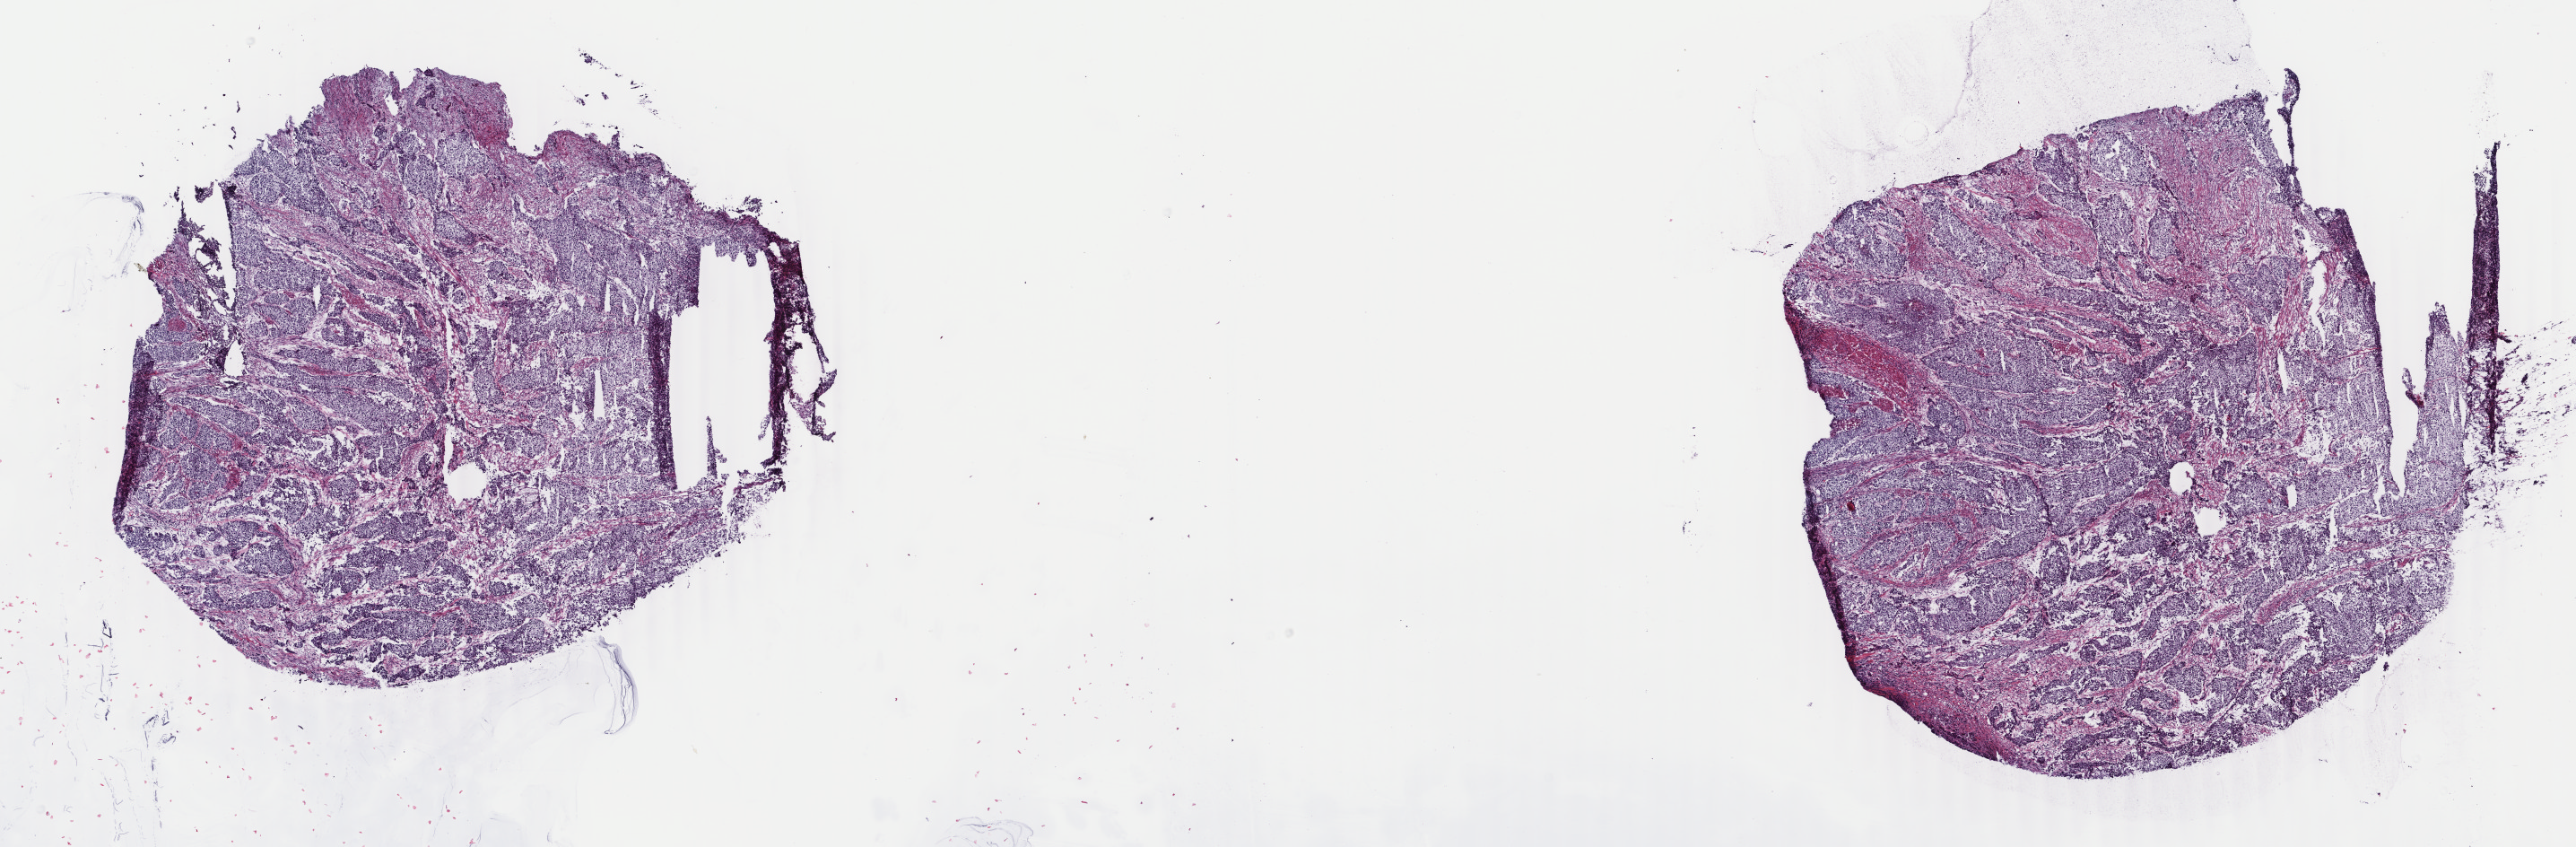
H&E-stained whole-slide image — shown as a low-resolution overview of the whole scanned area (about 22.8 x 7.5 mm, acquisition: 40x scan), frozen section from the top of the tissue portion, bladder, primary tumour sample. Female, age 82 years at initial diagnosis. Histologic grade: high grade. Pathologist review of this section (percent, as recorded): tumour cells 75%, tumour nuclei 75%, normal cells 12%, stromal cells 12%, necrosis 1%. Infiltration values recorded for this section: lymphocyte infiltration 2%, monocyte infiltration 0%, neutrophil infiltration 1%.
AJCC pathologic stage: III. Histologic diagnosis: Transitional cell carcinoma.